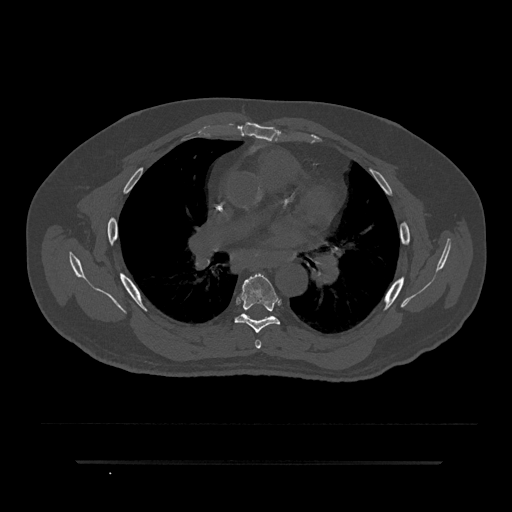
CT including the spine, one axial slice; slice 529 of 797 in the series (ordered by position); 120 kVp; bone window (W 1800 / L 400 HU); 0.5 mm slice thickness; 512 × 512 image matrix, field of view 464 × 464 mm. Male patient, age 59 years. From the clinical record (not read from this slice): primary cancer: bile ducts.
Annotated regions visible in this slice (semi-automatic segmentation, software-assisted and operator-edited):
- T5 vertebra: bounding box <255,339,261,349> (left, top, right, bottom; pixels)
- T6 vertebra: <234,274,281,333>